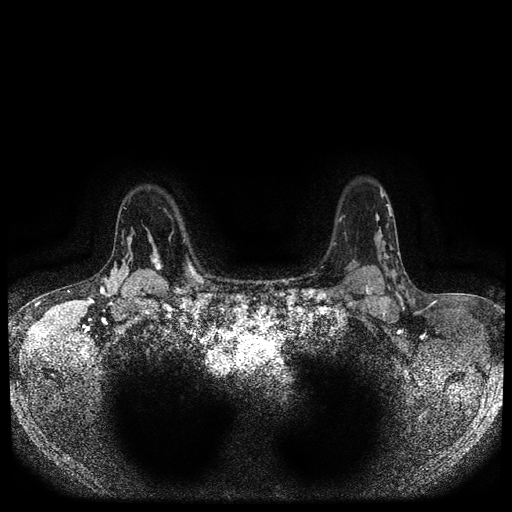
Breast MRI (dynamic contrast-enhanced, multi-phase), one axial slice. Position 79 of 116 along the scan axis. Dynamic contrast-enhanced series, time point 2 of 5 at this slice position (early post-contrast). 1.5 T. TE 2.6 ms, TR 5.4 ms. 2 mm slice thickness. 512 × 512 image matrix, field of view 340 × 340 mm. Female patient, age 47 years.
Structures marked on this image (semi-automatic segmentation, software-assisted and operator-edited):
- breast lesion (labelled 'tumour' in the annotation; benign lesions carry a separate 'benign' label): bounding box [x1, y1, x2, y2] px = [147, 235, 163, 274]